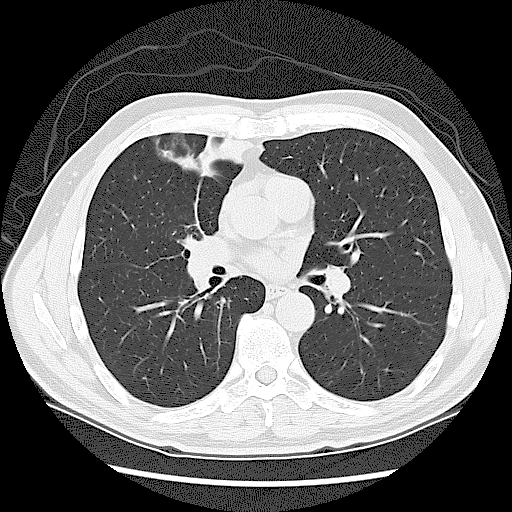
Axial slice from a low-dose chest CT screening exam, baseline screening round, lung window (W 1500 / L -600 HU), slice 65 of 131 in the series. Male participant, aged 60 years at enrolment.
Expert reader's lesion annotation, box from (x=158, y=213) to (x=239, y=302) px. Screening reader's record for this exam: no non-calcified nodule ≥4 mm recorded. Lung cancer was diagnosed 41 days after this screen: small cell carcinoma, NOS, right upper lobe, stage IIIA (AJCC 6th edition).